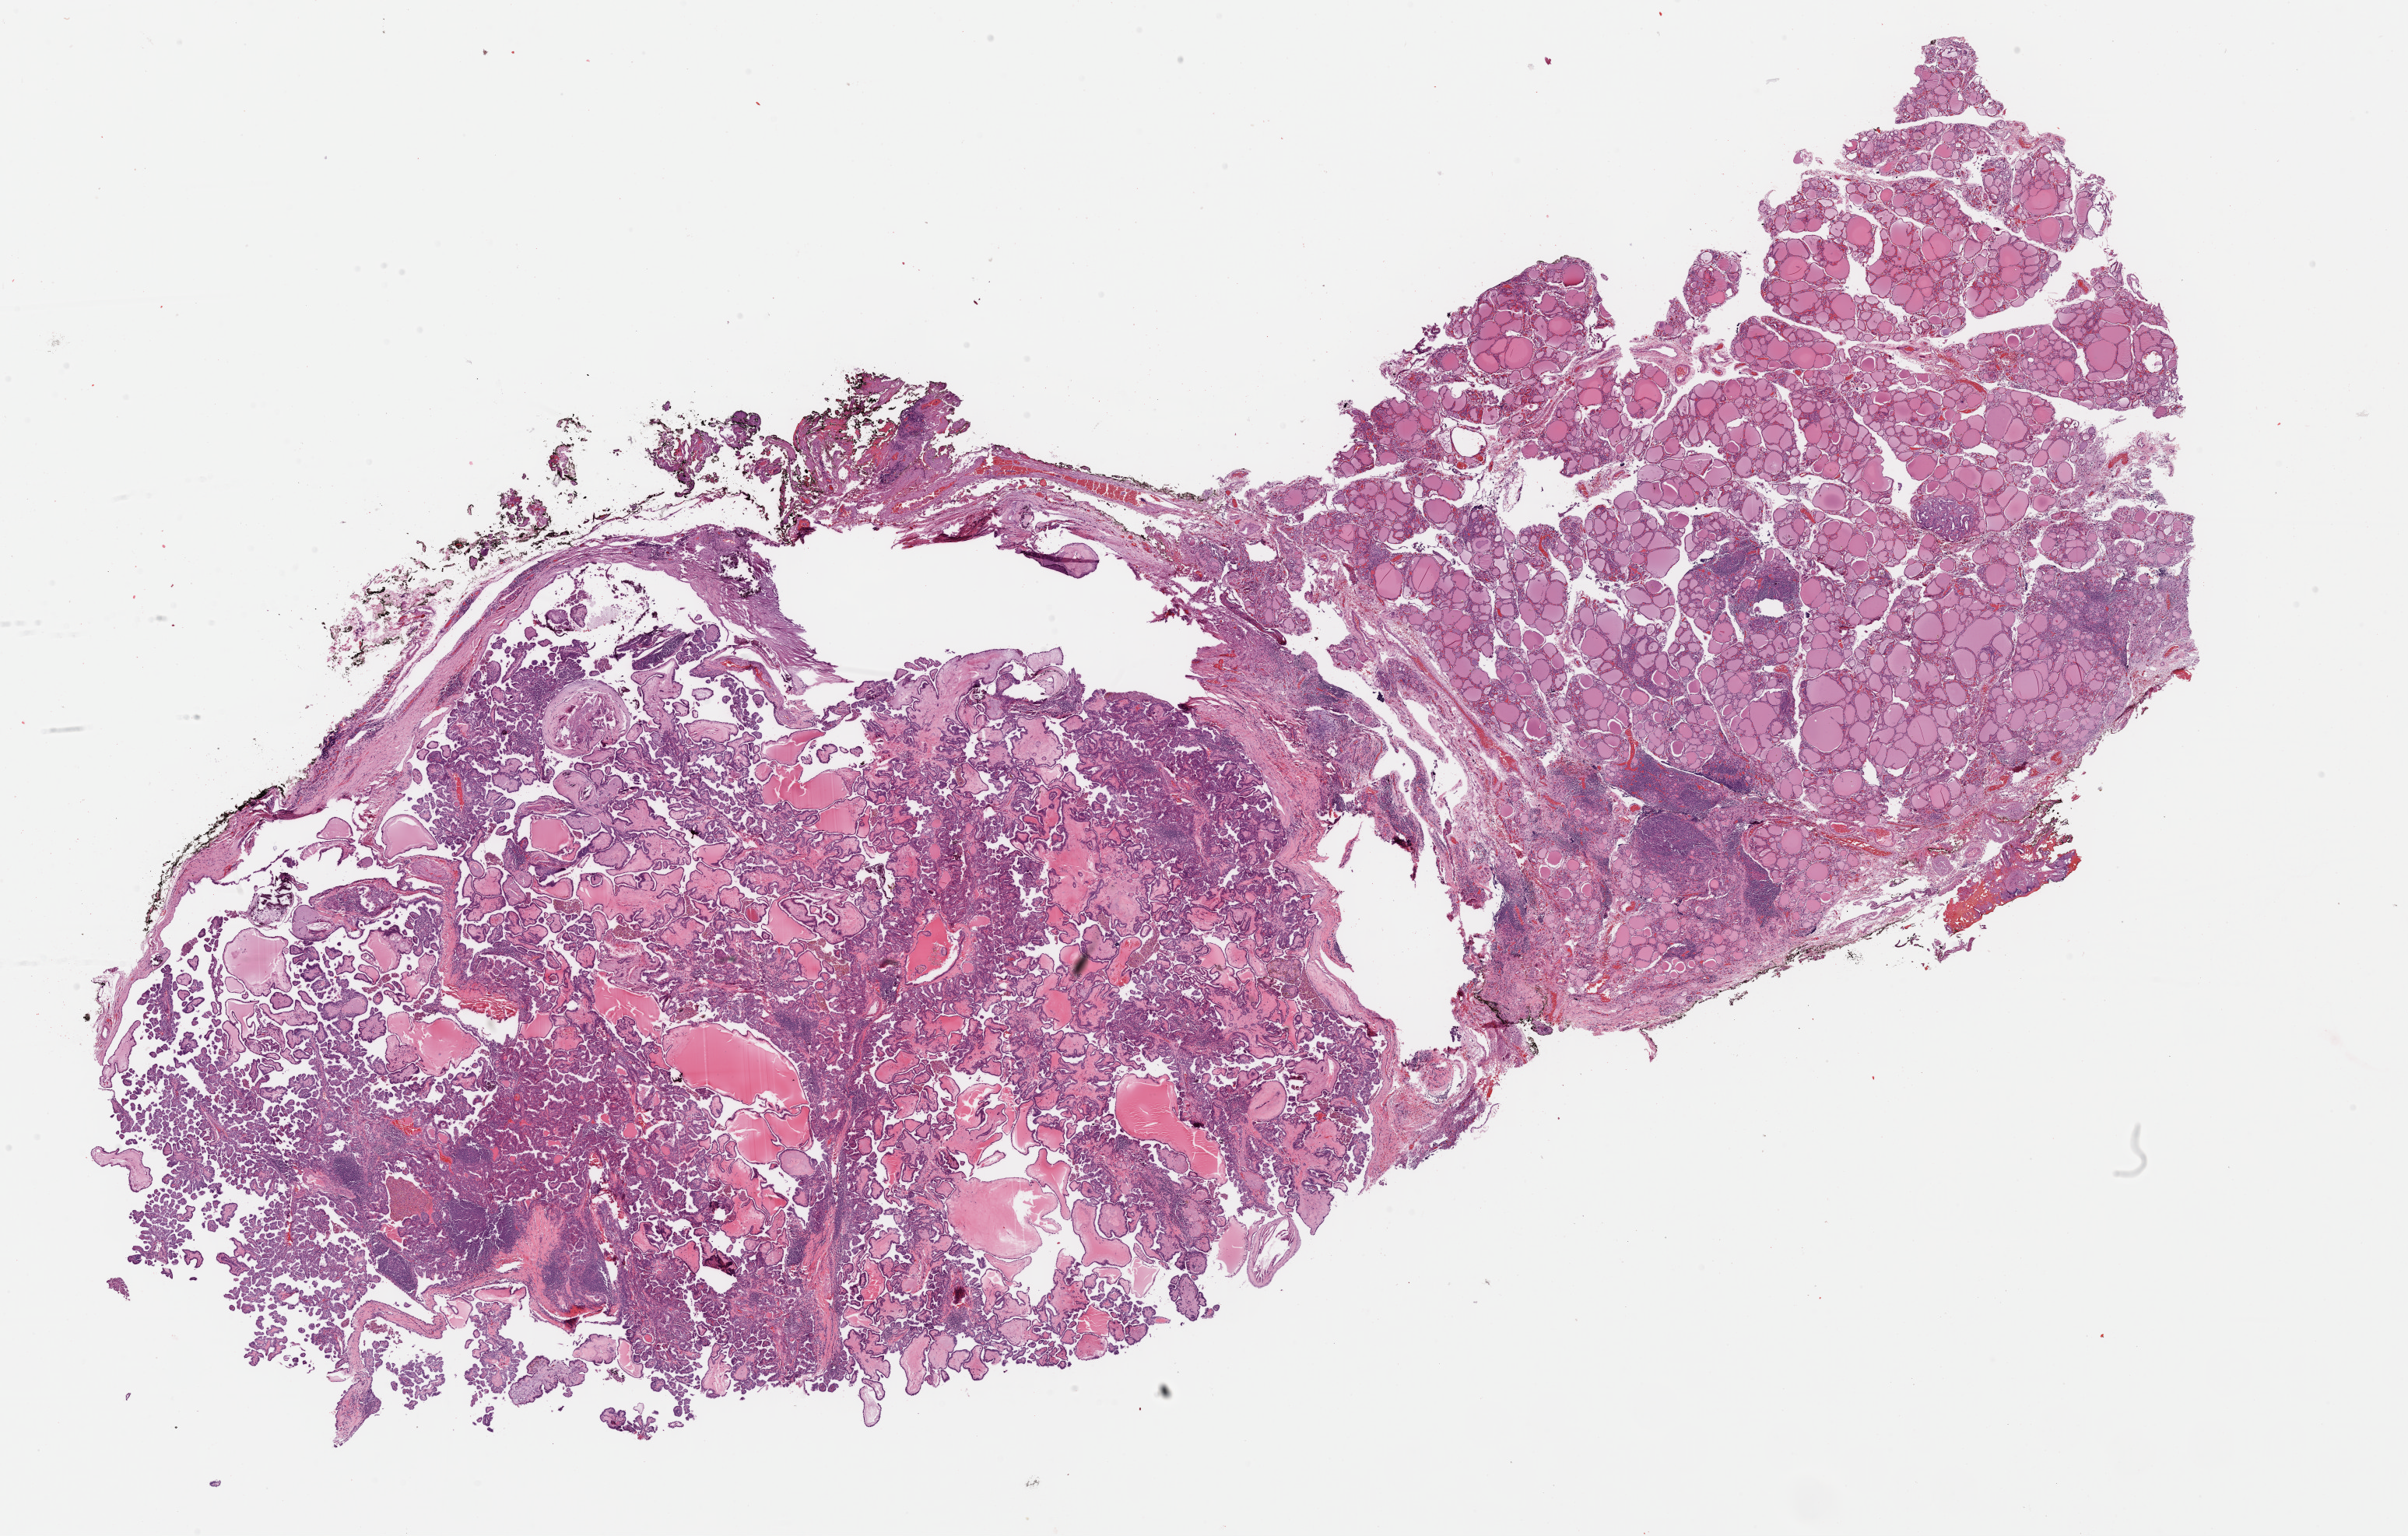
Whole-slide histology image, Hematoxylin and eosin (H&E) stained, whole scanned area (about 24.4 x 15.6 mm) shown as a low-resolution overview; FFPE section; primary tumour sample from the thyroid. Female, age 58 years at initial diagnosis.
* AJCC pathologic stage: I (6th edition)
* pathologic diagnosis: Papillary adenocarcinoma, NOS (thyroid gland)